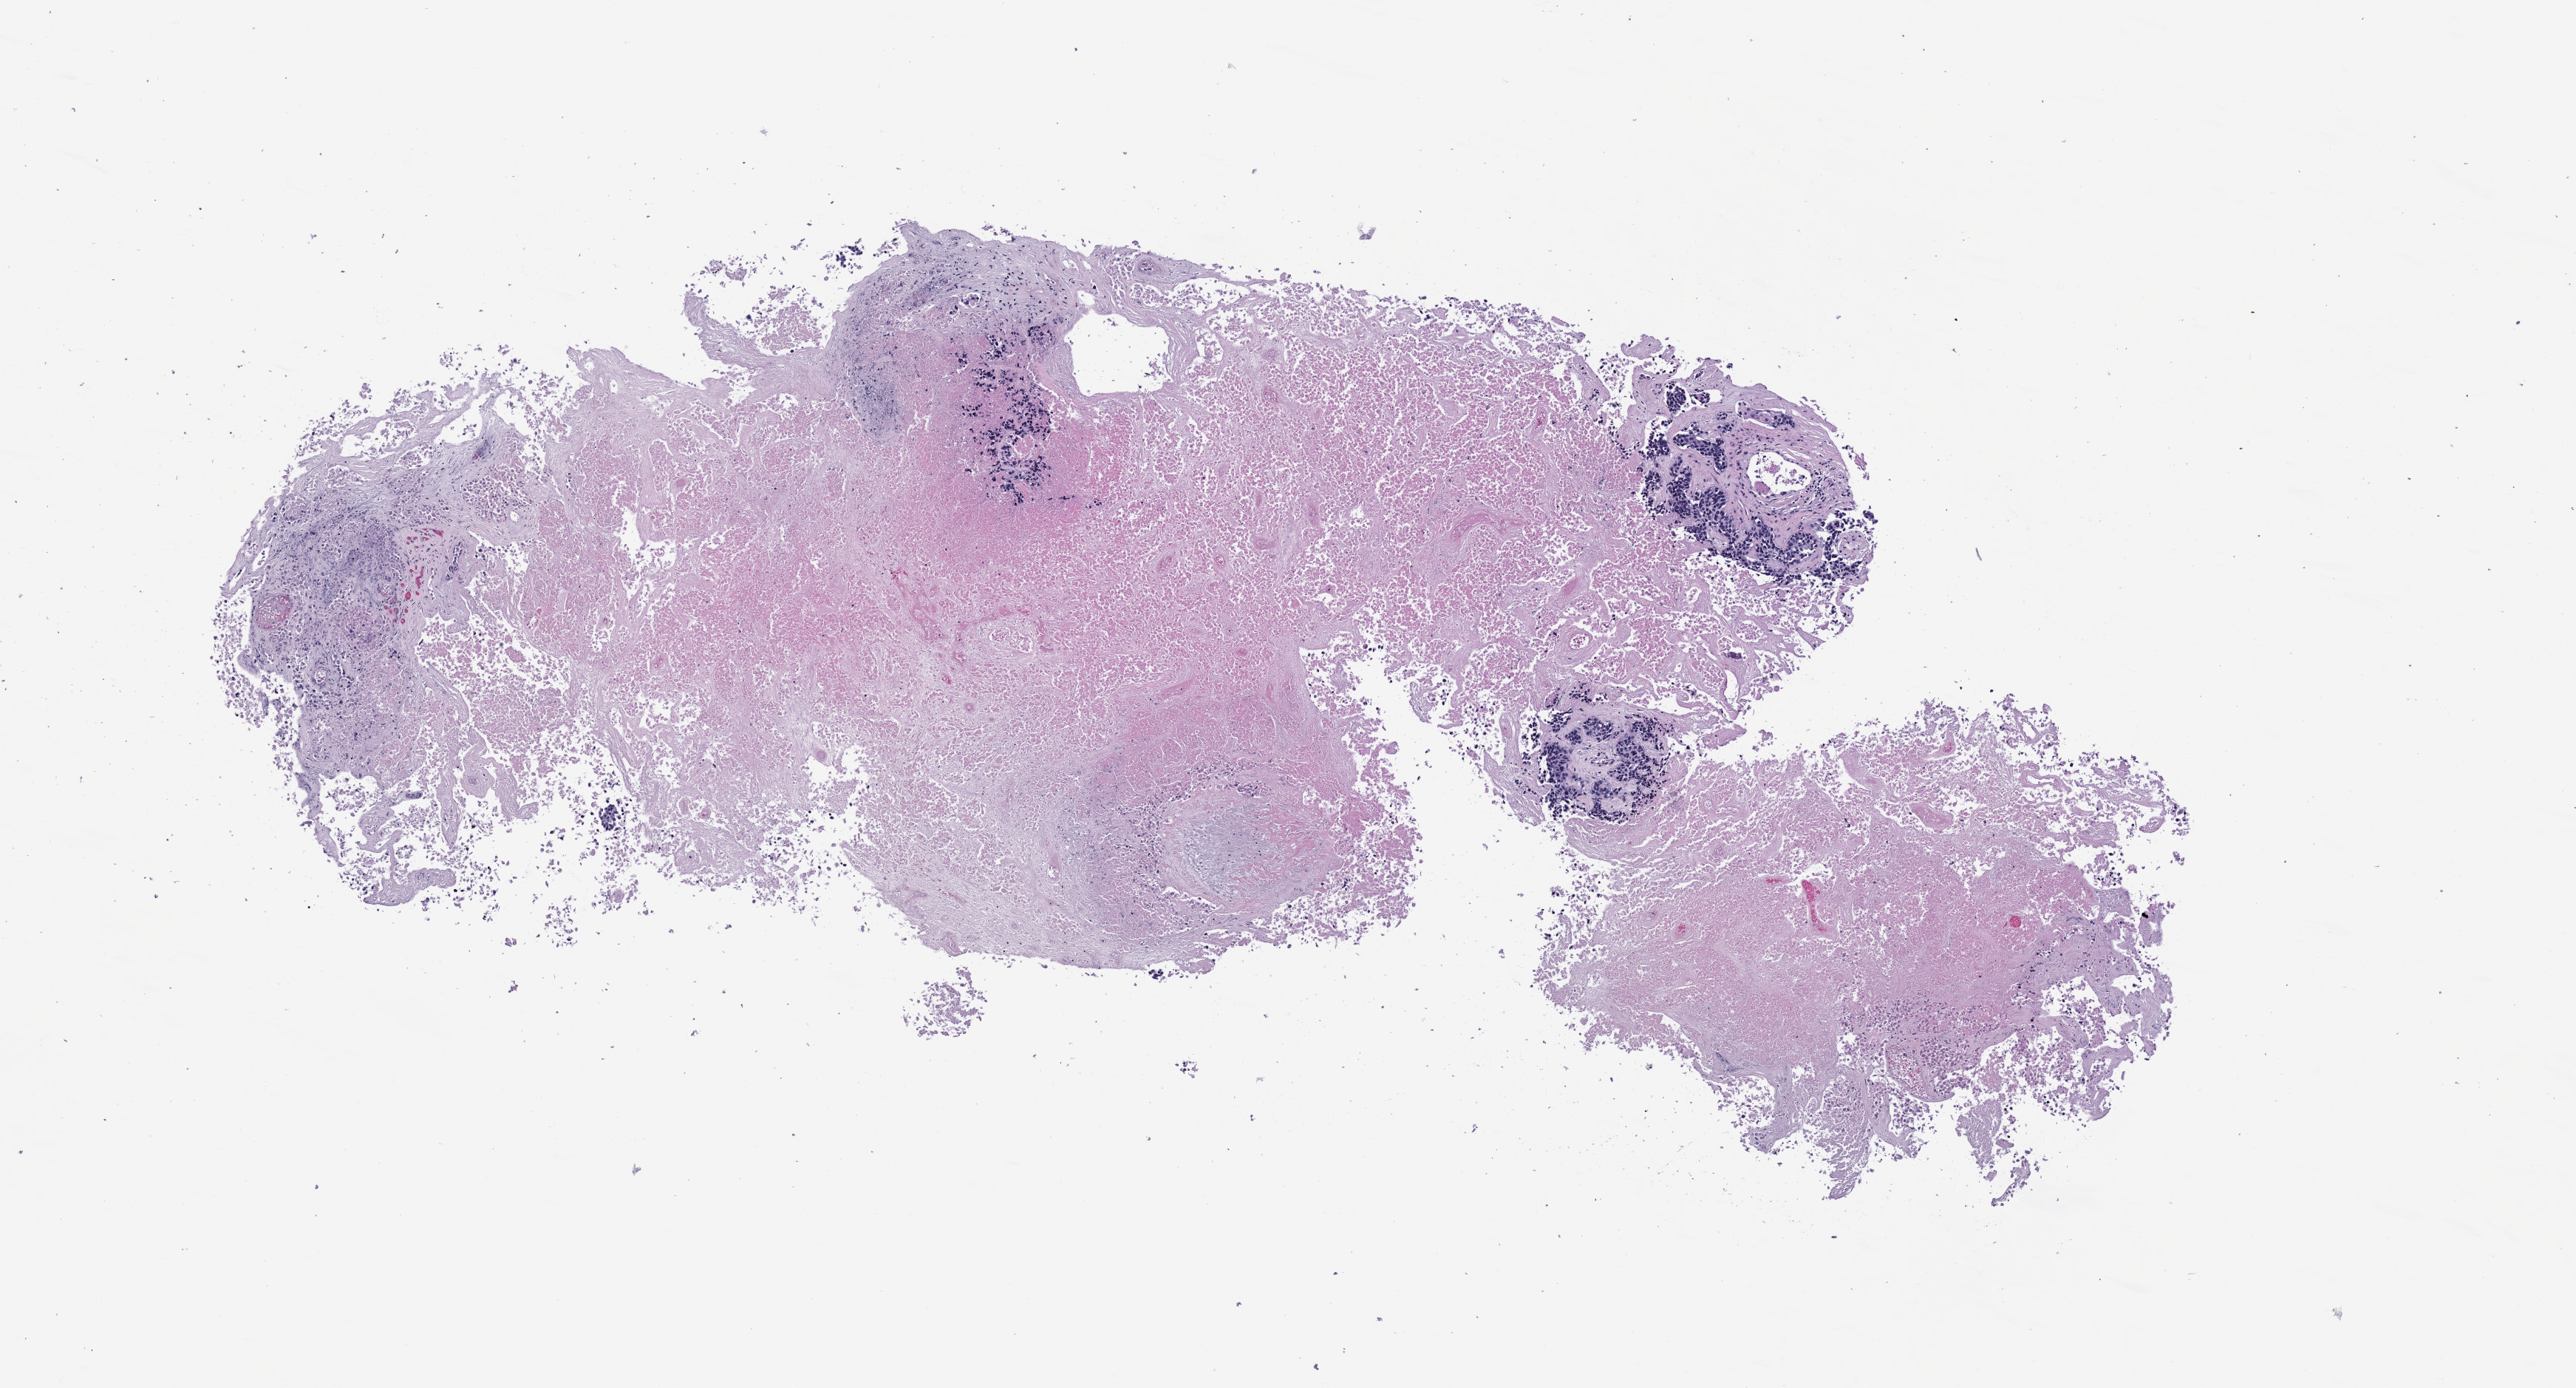
Whole-slide image, H&E stain of the patient's (originator) tumor tissue, whole scanned area (about 7.0 x 3.8 mm) shown as a low-resolution overview. Formalin-fixed paraffin-embedded section. Tumor site category: lung. Patient male; aged 55.
Diagnosis: Lung Squamous Cell Carcinoma.